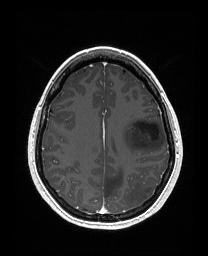
Brain MRI from a brain-tumour surgery series, one axial slice. Position 112 of 176 along the scan axis. T1-weighted post-contrast. 1 mm slice thickness. 208 × 256 image matrix. From the clinical record (not read from this slice): histopathology: Astrocytoma; WHO grade: 3; IDH mutation: yes; tumour location: Left Frontal.
Annotated regions visible in this slice (outlined manually by an expert reader):
- tumour: bounding box [x1, y1, x2, y2] px = [121, 118, 165, 154]